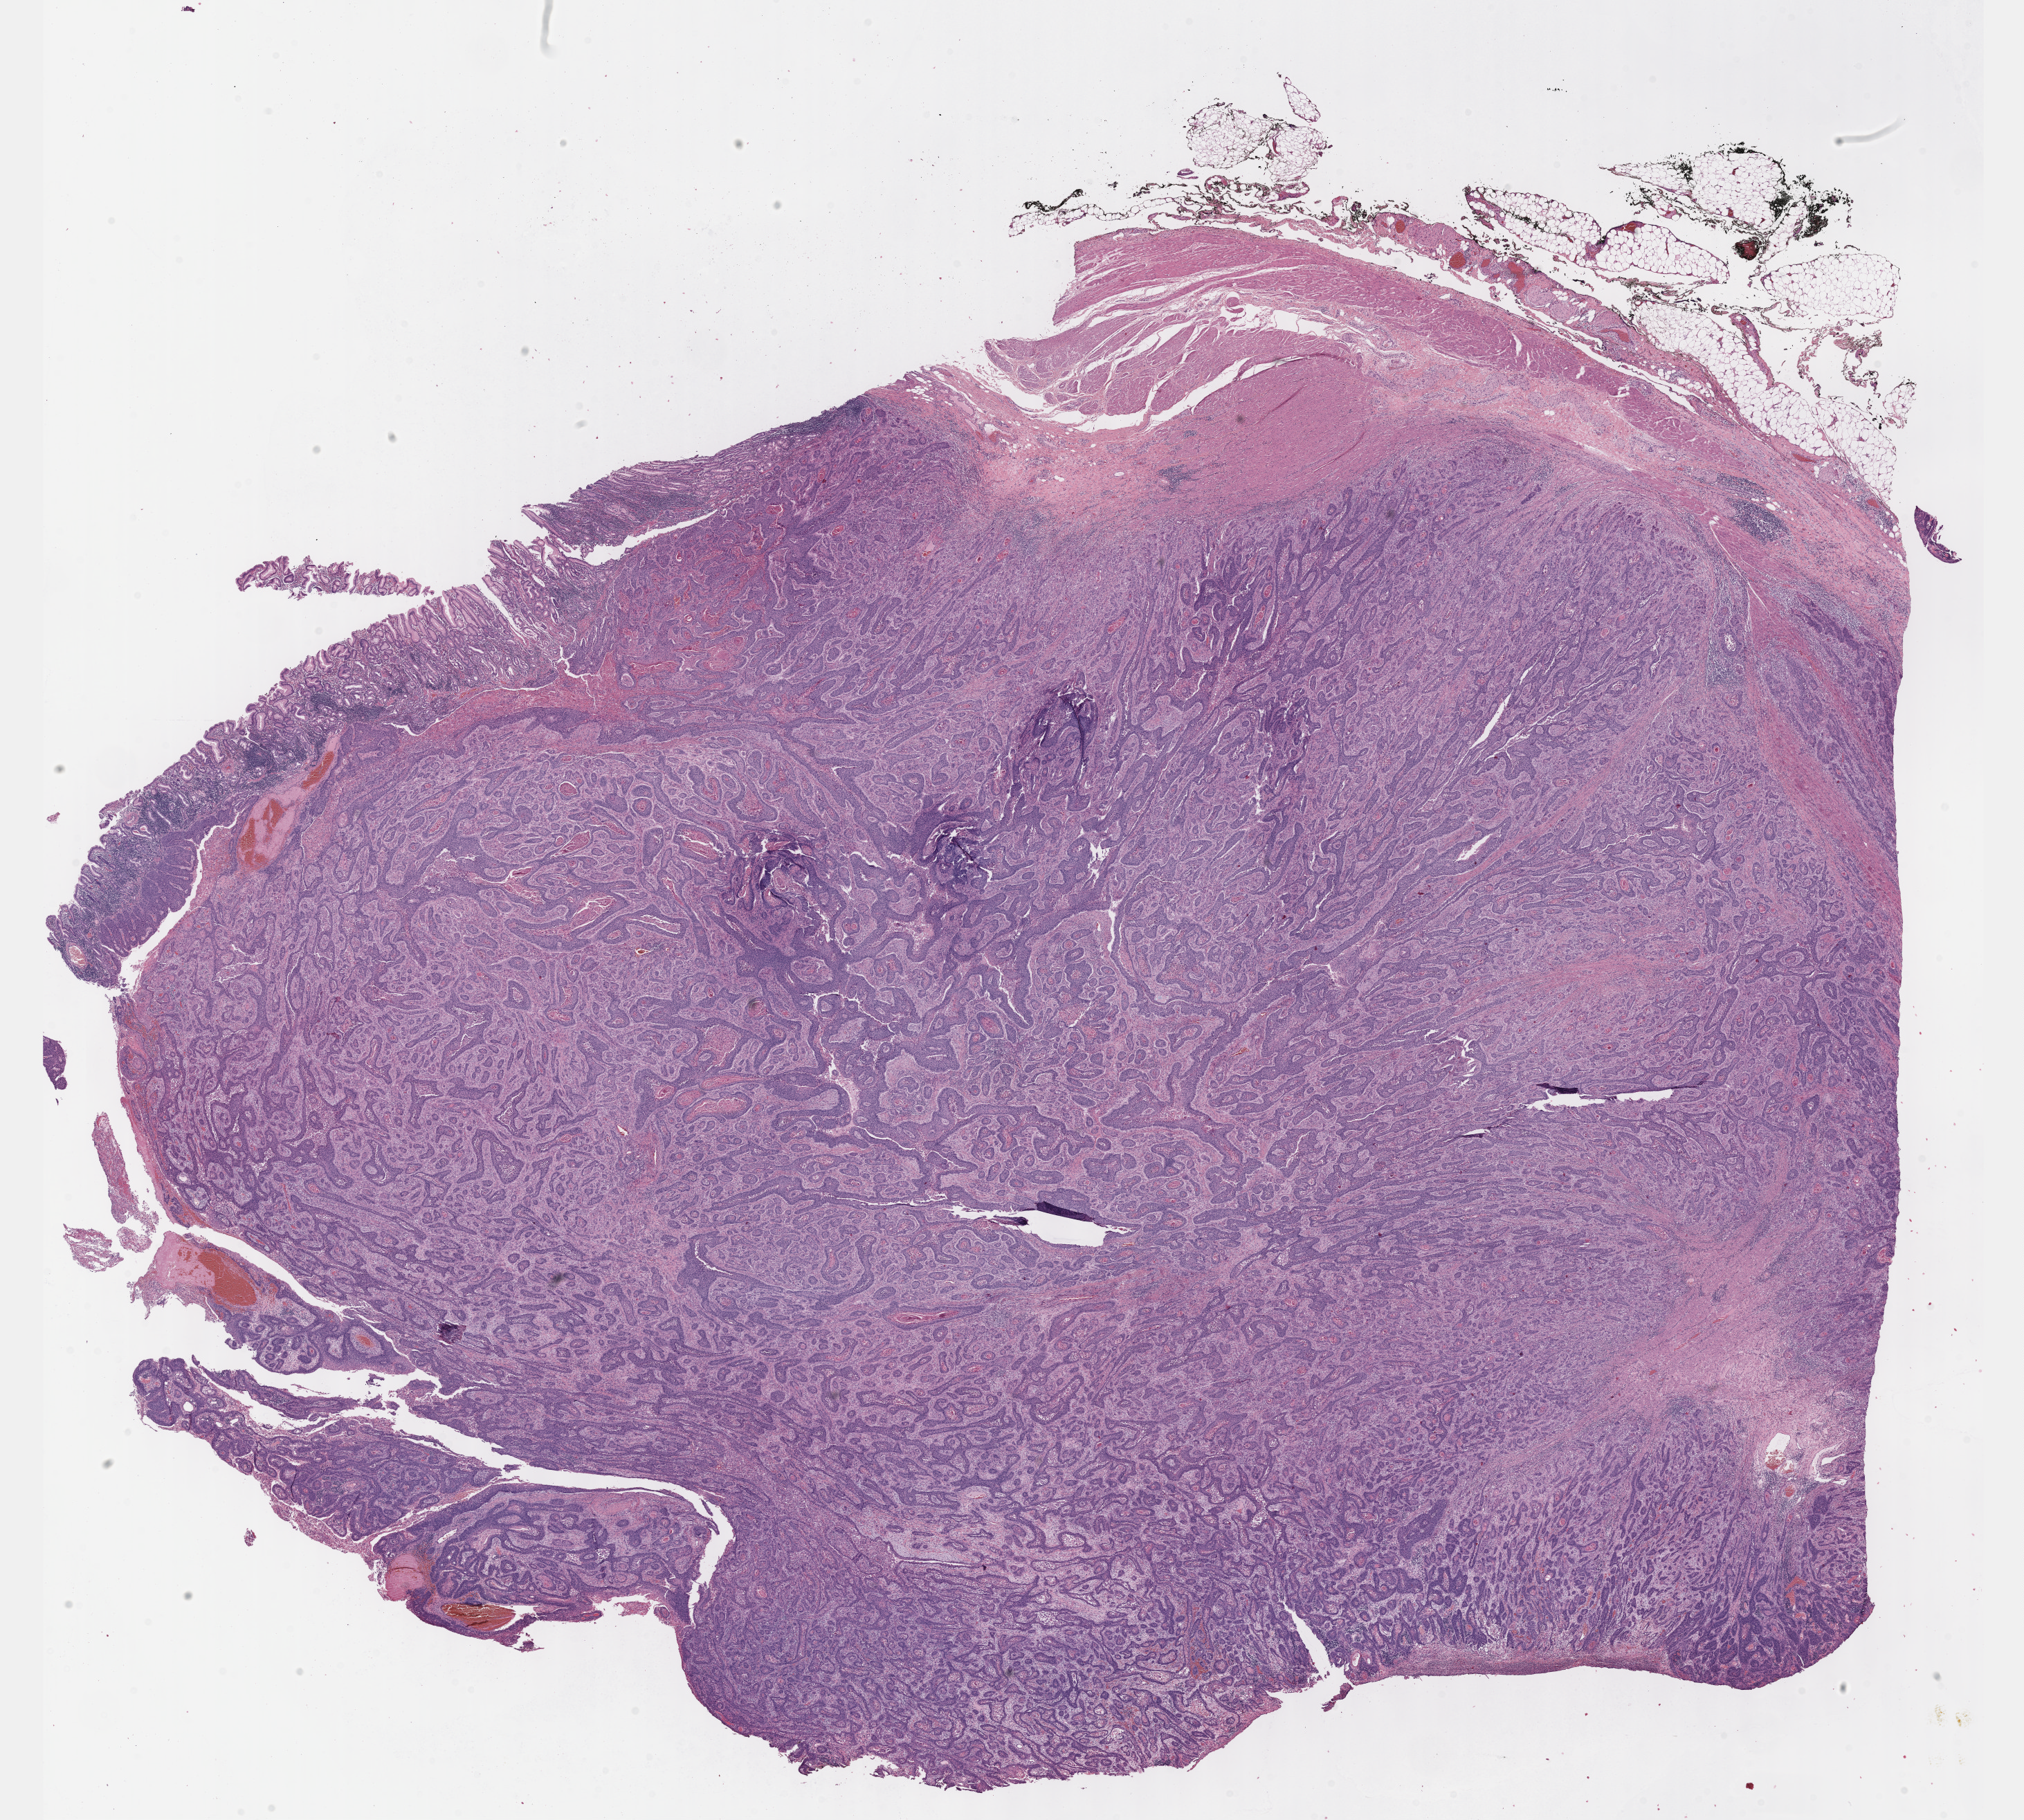
Digitized H&E tissue section (whole slide), whole scanned area (about 23.6 x 21.3 mm, from a 40x scan) shown as a low-resolution overview; formalin-fixed paraffin-embedded (FFPE) diagnostic section; sample: primary tumour, esophagus. Female patient; age at initial diagnosis 44 years. Histologic grade: G1 (well differentiated).
- diagnosis: Squamous cell carcinoma, NOS (lower third of esophagus)
- AJCC pathologic stage: IIA (7th edition)
- lymph nodes positive (case pathology): 0 of 32 examined